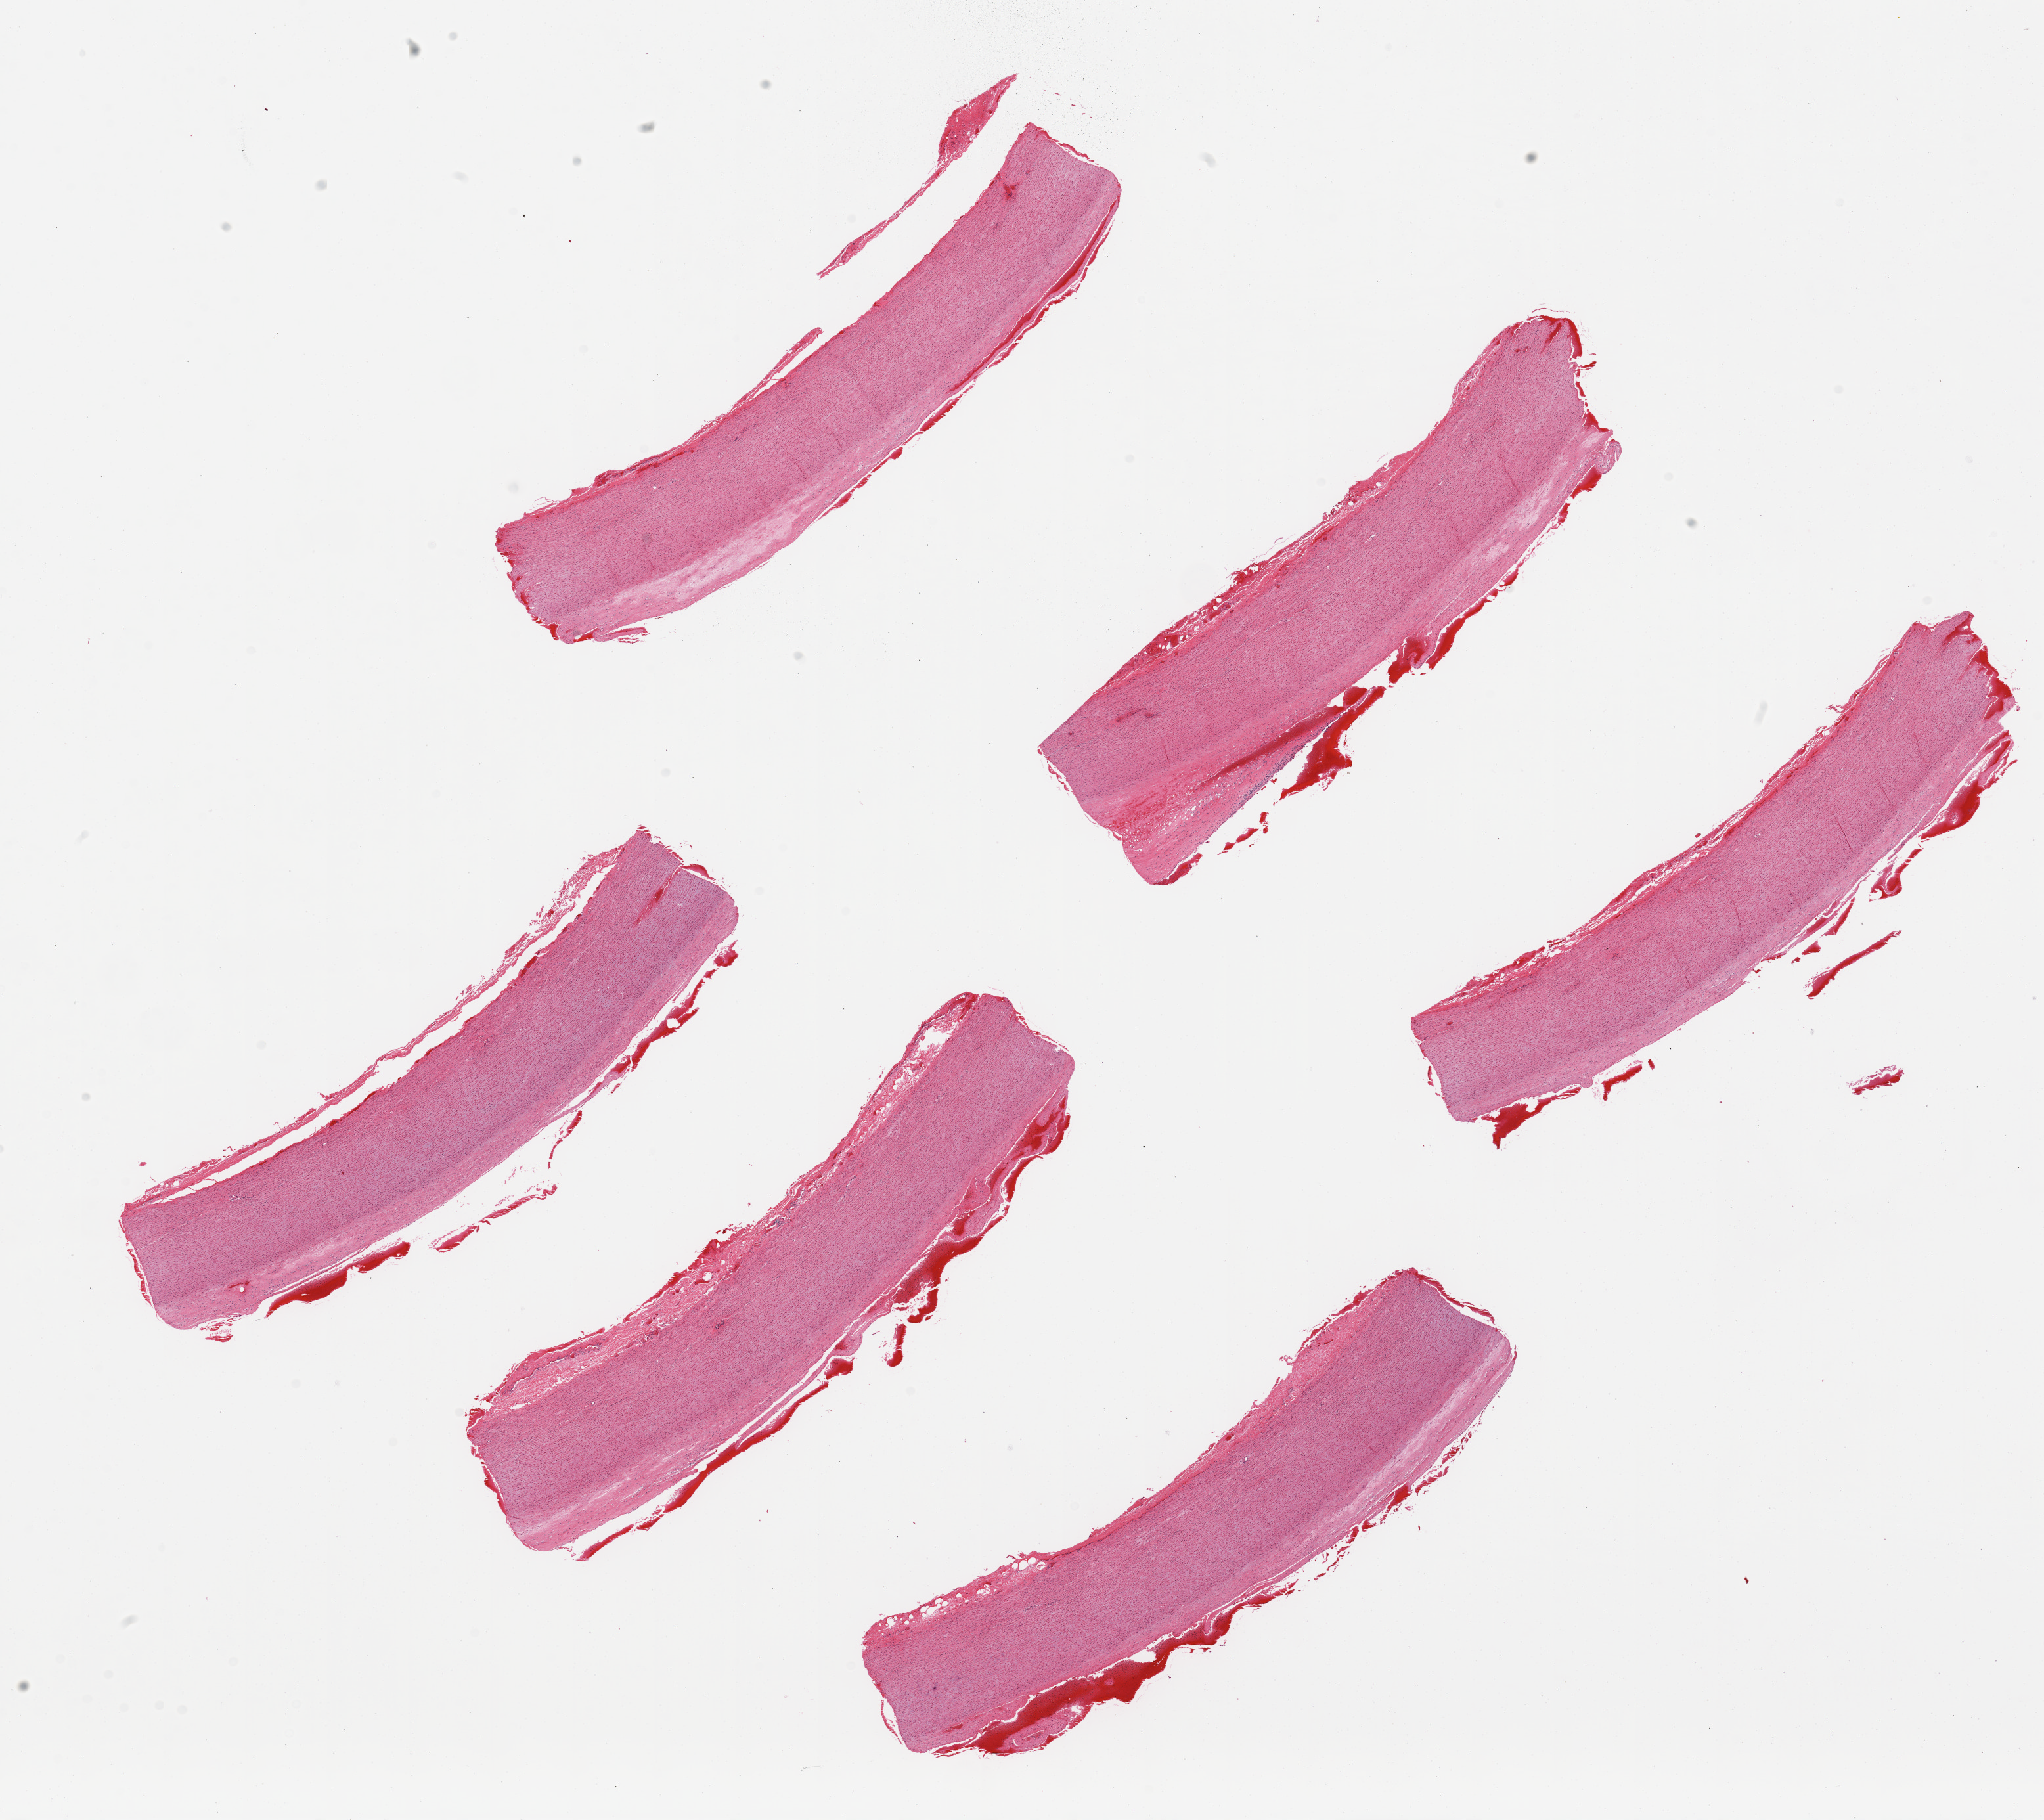
H&E whole-slide image, brightfield — whole scanned area (about 24.6 x 21.9 mm) shown as a low-resolution overview; PAXgene-fixed, paraffin-embedded tissue; section of aorta (target tissue); tissue donor sample. Donor: male.
Review note (as recorded): 6 pieces, atherosis layer up to ~0.3mm.